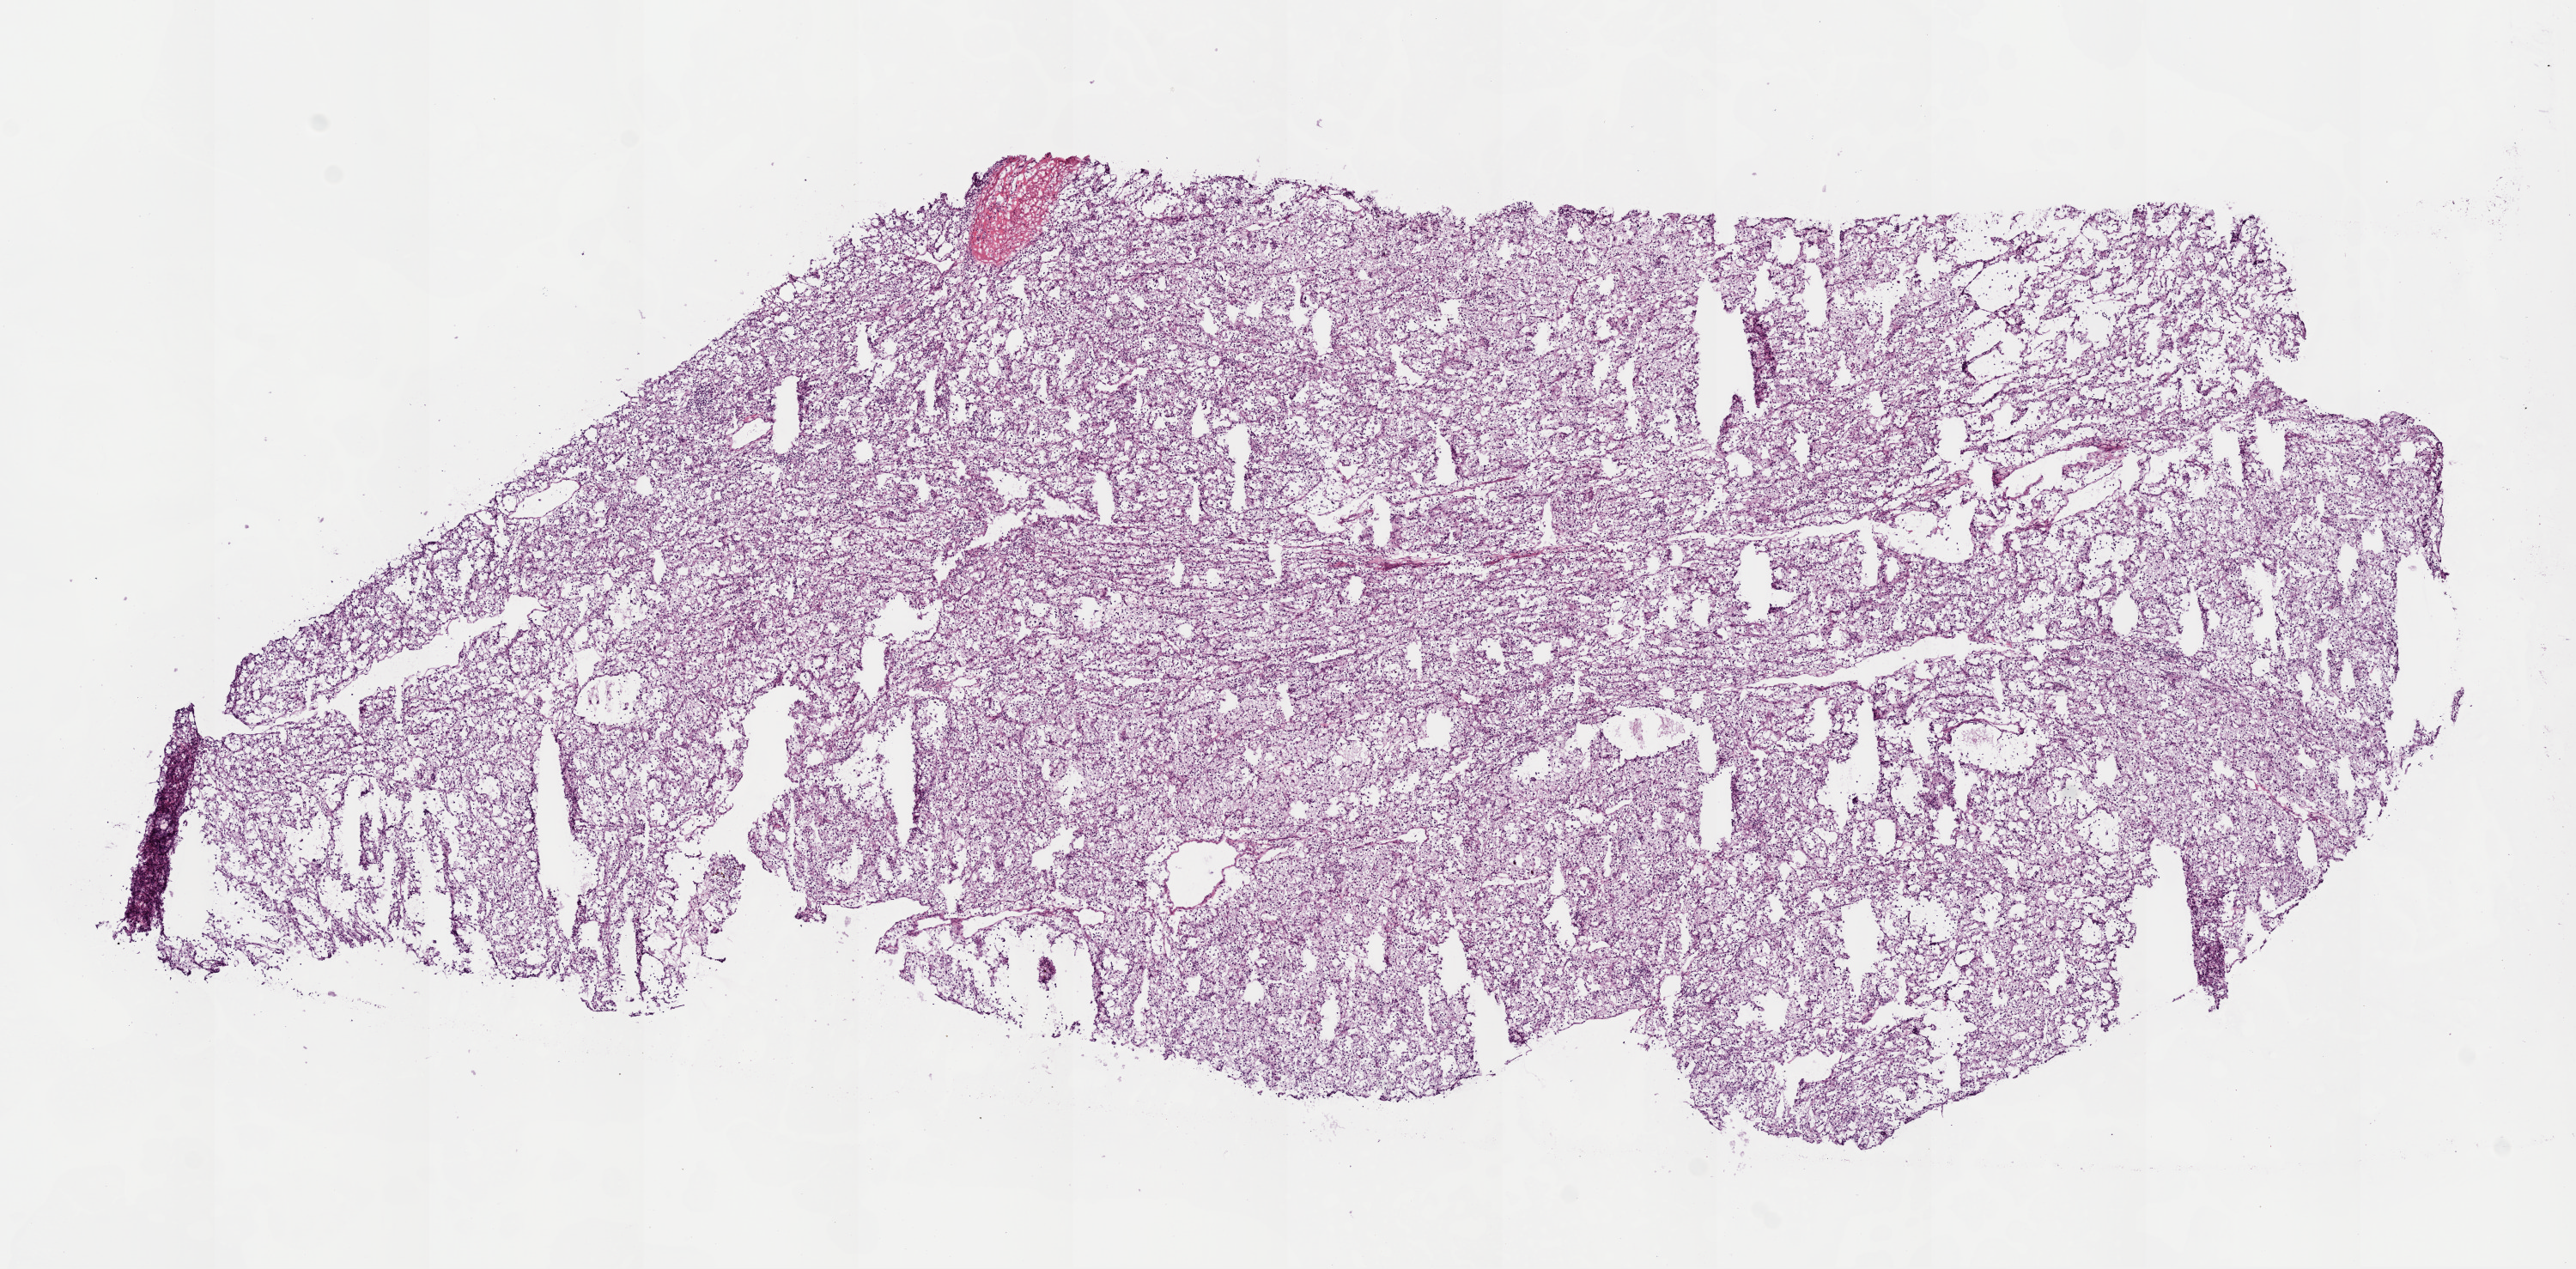
Digitized Hematoxylin and eosin (H&E) stained tissue section (whole slide) — shown as a low-resolution overview of the whole scanned area (about 12.0 x 5.9 mm, slide scanned at 20x). Frozen section. Sample: primary tumour, kidney. Female, age 62 years at initial diagnosis. Histologic grade: G2 (moderately differentiated). Pathologist review of this section (percent, as recorded): tumour cells 95%, tumour nuclei 90%, normal cells 0%, stromal cells 5%, necrosis 0%.
Histologic diagnosis: Clear cell adenocarcinoma, NOS. AJCC pathologic stage: III.